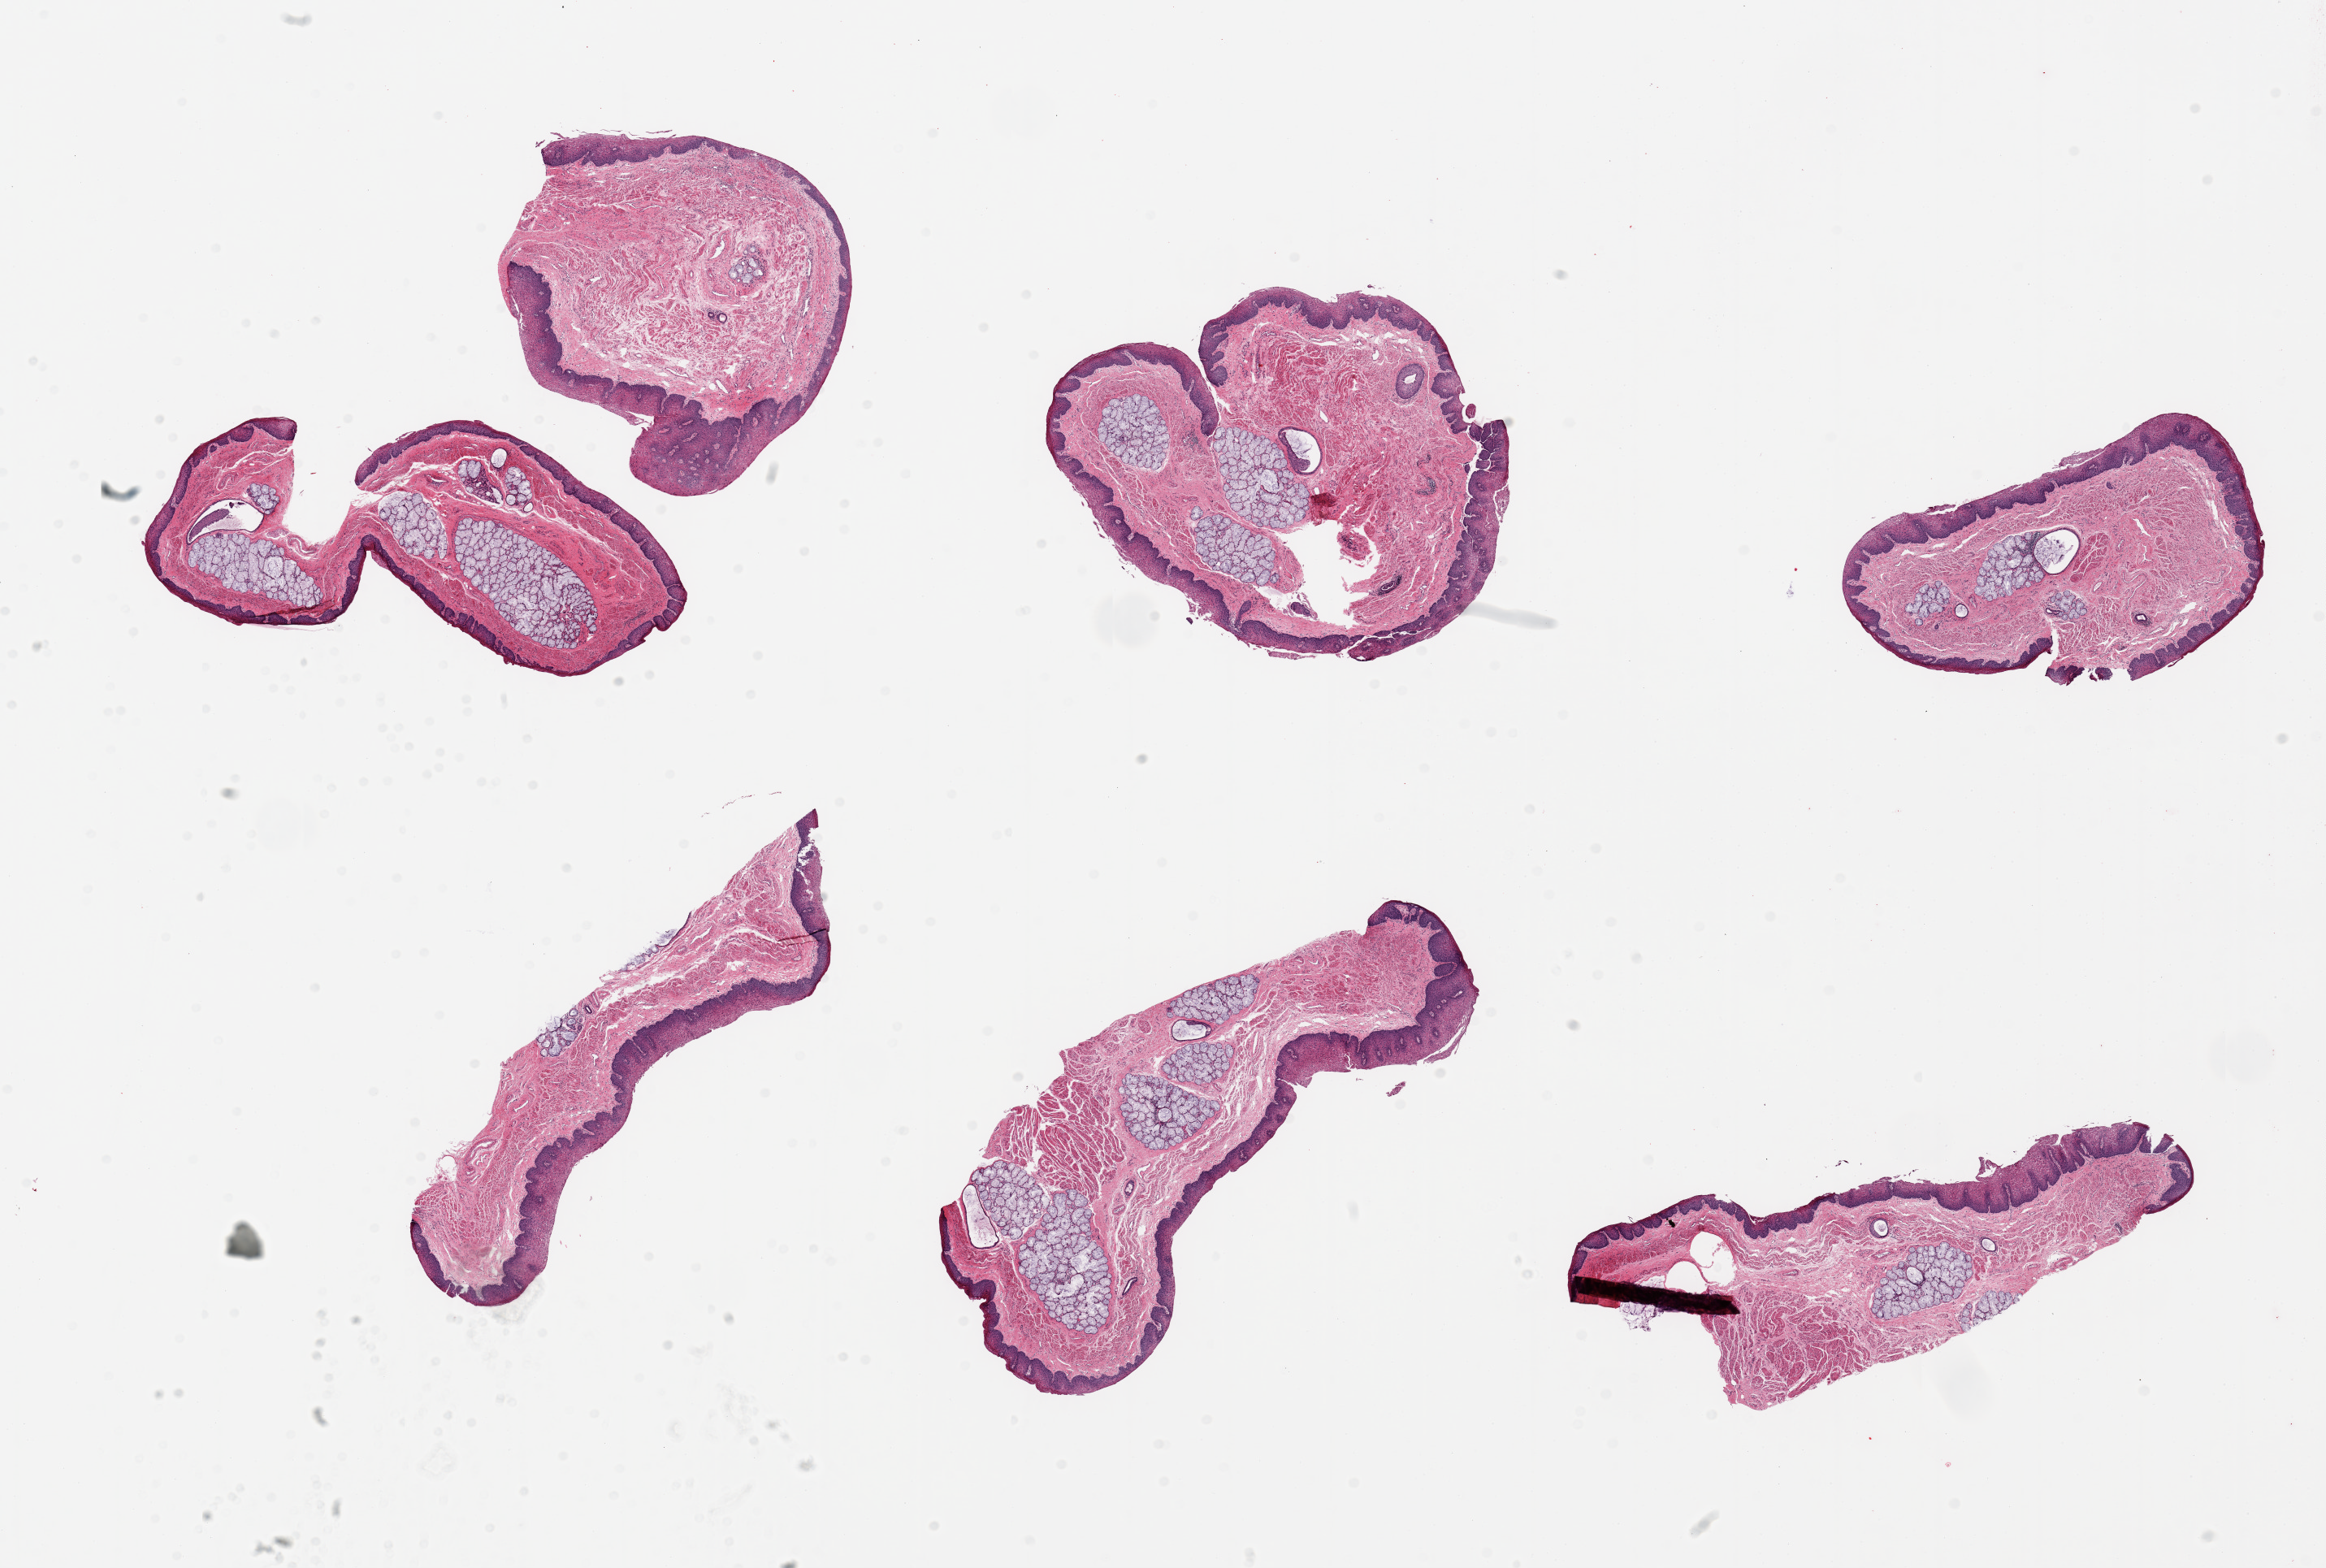
Whole-slide image, hematoxylin and eosin (H&E) stain, whole scanned area (about 22.6 x 15.3 mm, from a 20x scan) shown as a low-resolution overview, PAXgene-fixed paraffin-embedded (PFPE) section, sampled site (target tissue): esophageal mucous membrane, tissue donor sample. Donor sex: male.
Review note (as recorded): 7 pieces; prominent submucosal glands comprise 5% to 50%.